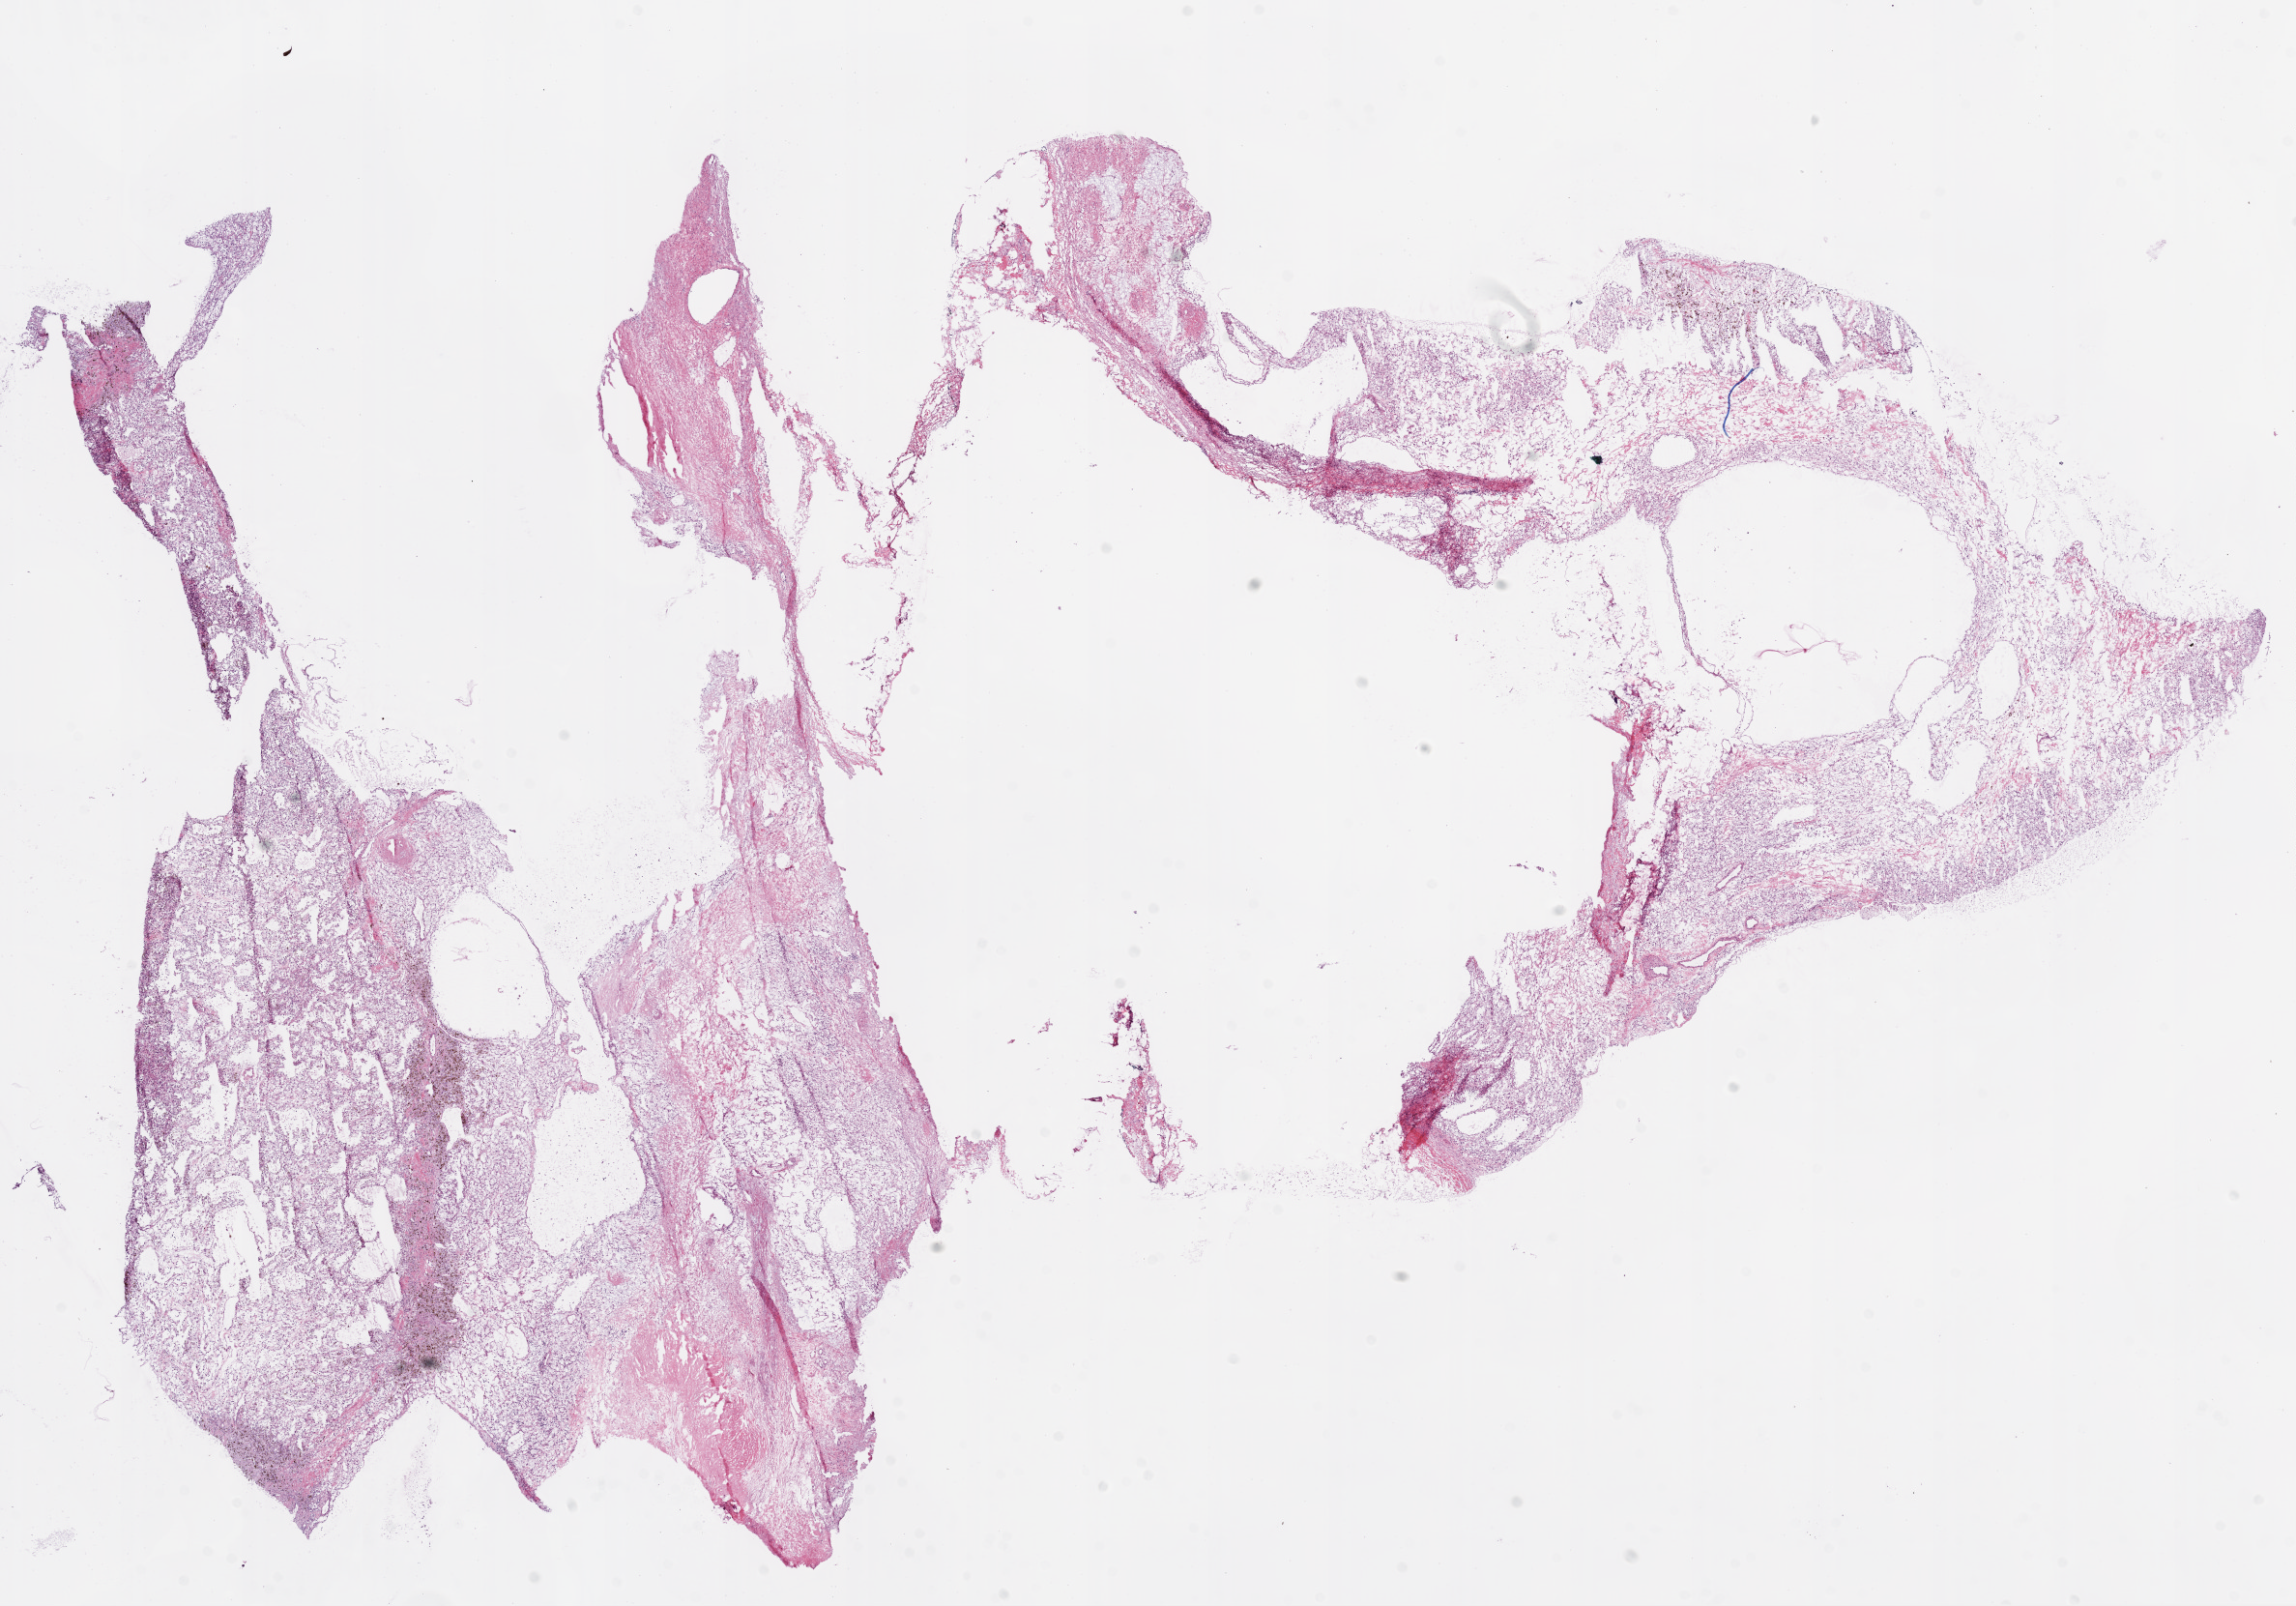
Digitized Hematoxylin and eosin (H&E) stained tissue section (whole slide), shown as a low-resolution overview of the whole scanned area (about 19.1 x 13.3 mm). Frozen section. Kidney, primary tumour sample. Male patient; age at initial diagnosis 57 years. Histologic grade: G2 (moderately differentiated). Pathologist review of this section (percent, as recorded): tumour cells 90%, tumour nuclei 90%, normal cells 0%, stromal cells 10%, necrosis 0%.
- diagnosis: Clear cell adenocarcinoma, NOS
- AJCC pathologic stage: I
- laterality: left